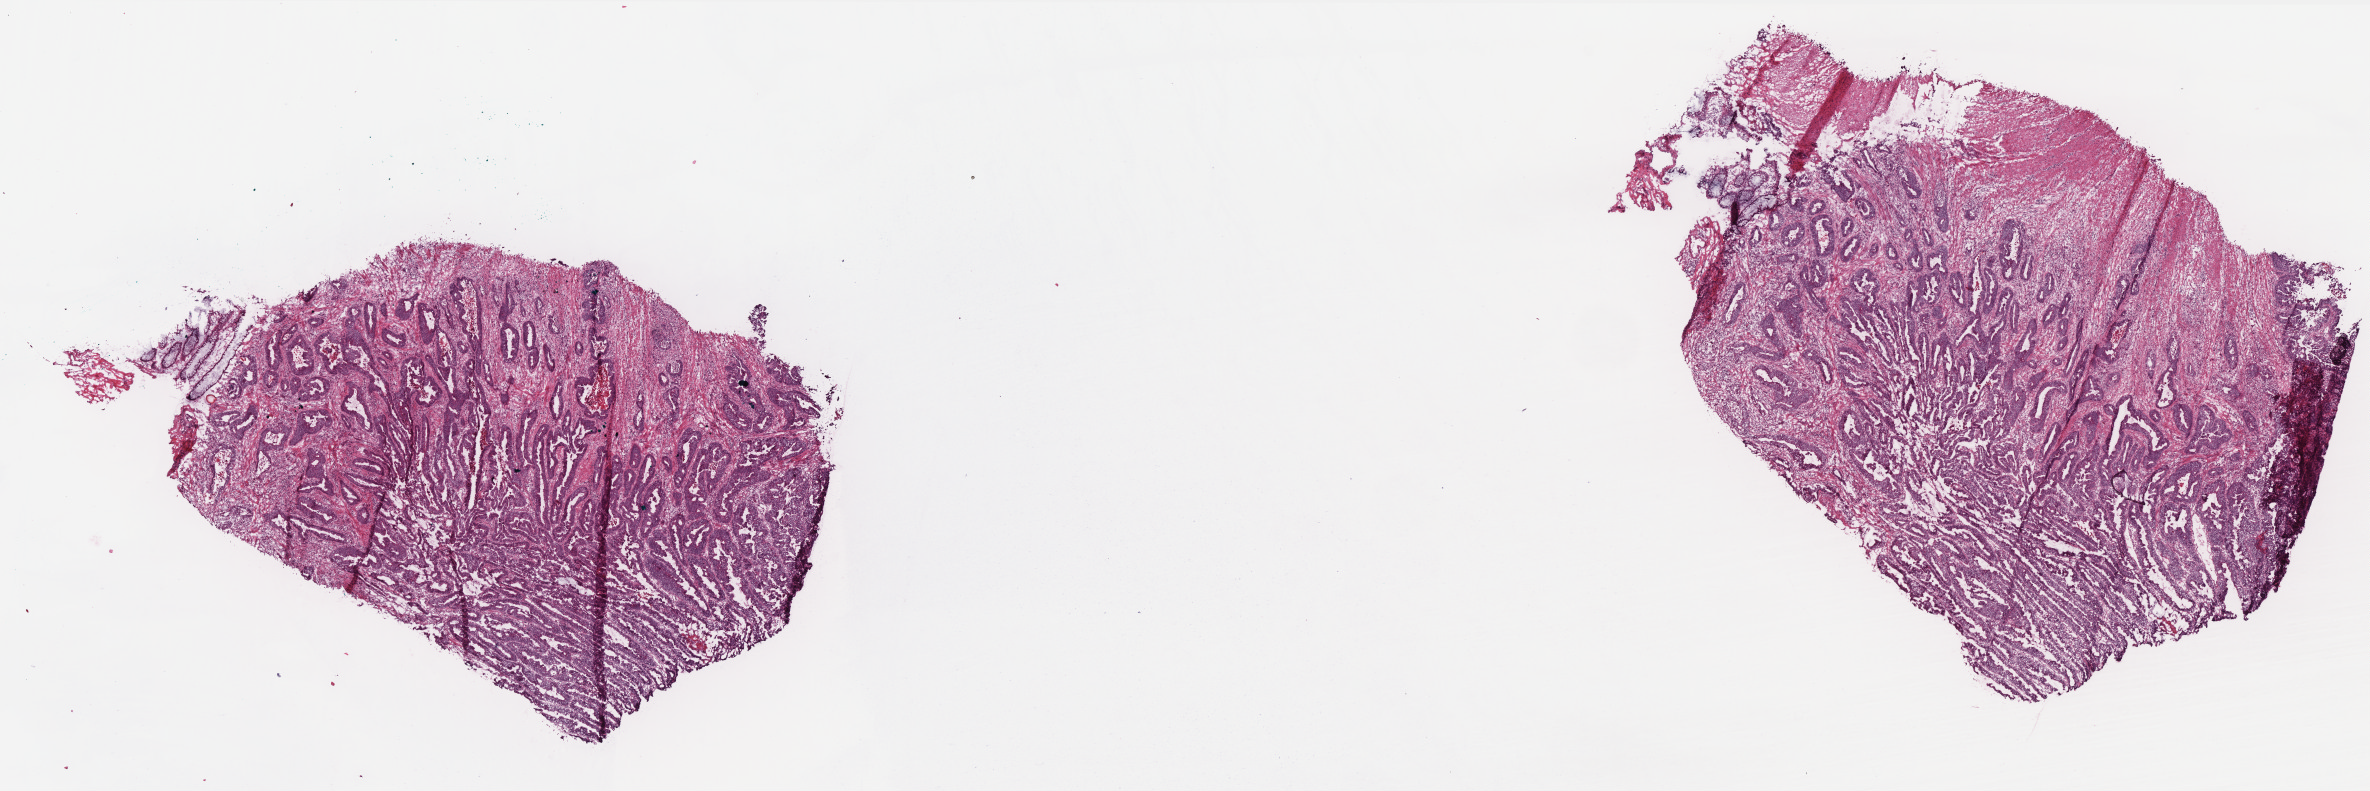
Whole-slide histology image, Hematoxylin and eosin (H&E) stained, whole scanned area (about 19.0 x 6.3 mm, acquisition: 40x scan) shown as a low-resolution overview; frozen section from the bottom of the tissue portion; sample: primary tumour, rectum. Patient: male, age at initial diagnosis 66 years. Composition of this section per pathologist review: tumour cells 75%, tumour nuclei 80%, normal cells 3%, stromal cells 20%, necrosis 2%. Inflammatory infiltration, as recorded: lymphocyte infiltration 3%, monocyte infiltration 0%, neutrophil infiltration 3%.
Lymph nodes positive (case pathology): 0 of 15 examined. Histologic diagnosis: Adenocarcinoma, NOS. AJCC pathologic stage: II (5th edition).